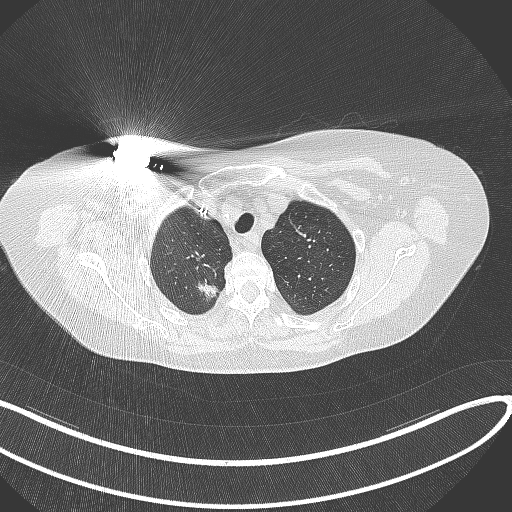
Chest CT, one axial slice; position 280 of 316 along the scan axis; reconstruction kernel B70f; 120 kVp; lung window (W 1500 / L -600 HU); 1 mm slice thickness; 512 × 512 image matrix, field of view 400 × 400 mm. Female patient, age 72 years. From the clinical record (not read from this slice): clinical TNM (as recorded): T1c N0 M0.
Structures marked on this image (rectangle marked by the reading radiologist):
- lung tumour (recorded histology: adenocarcinoma): box from (x=192, y=271) to (x=219, y=303) px